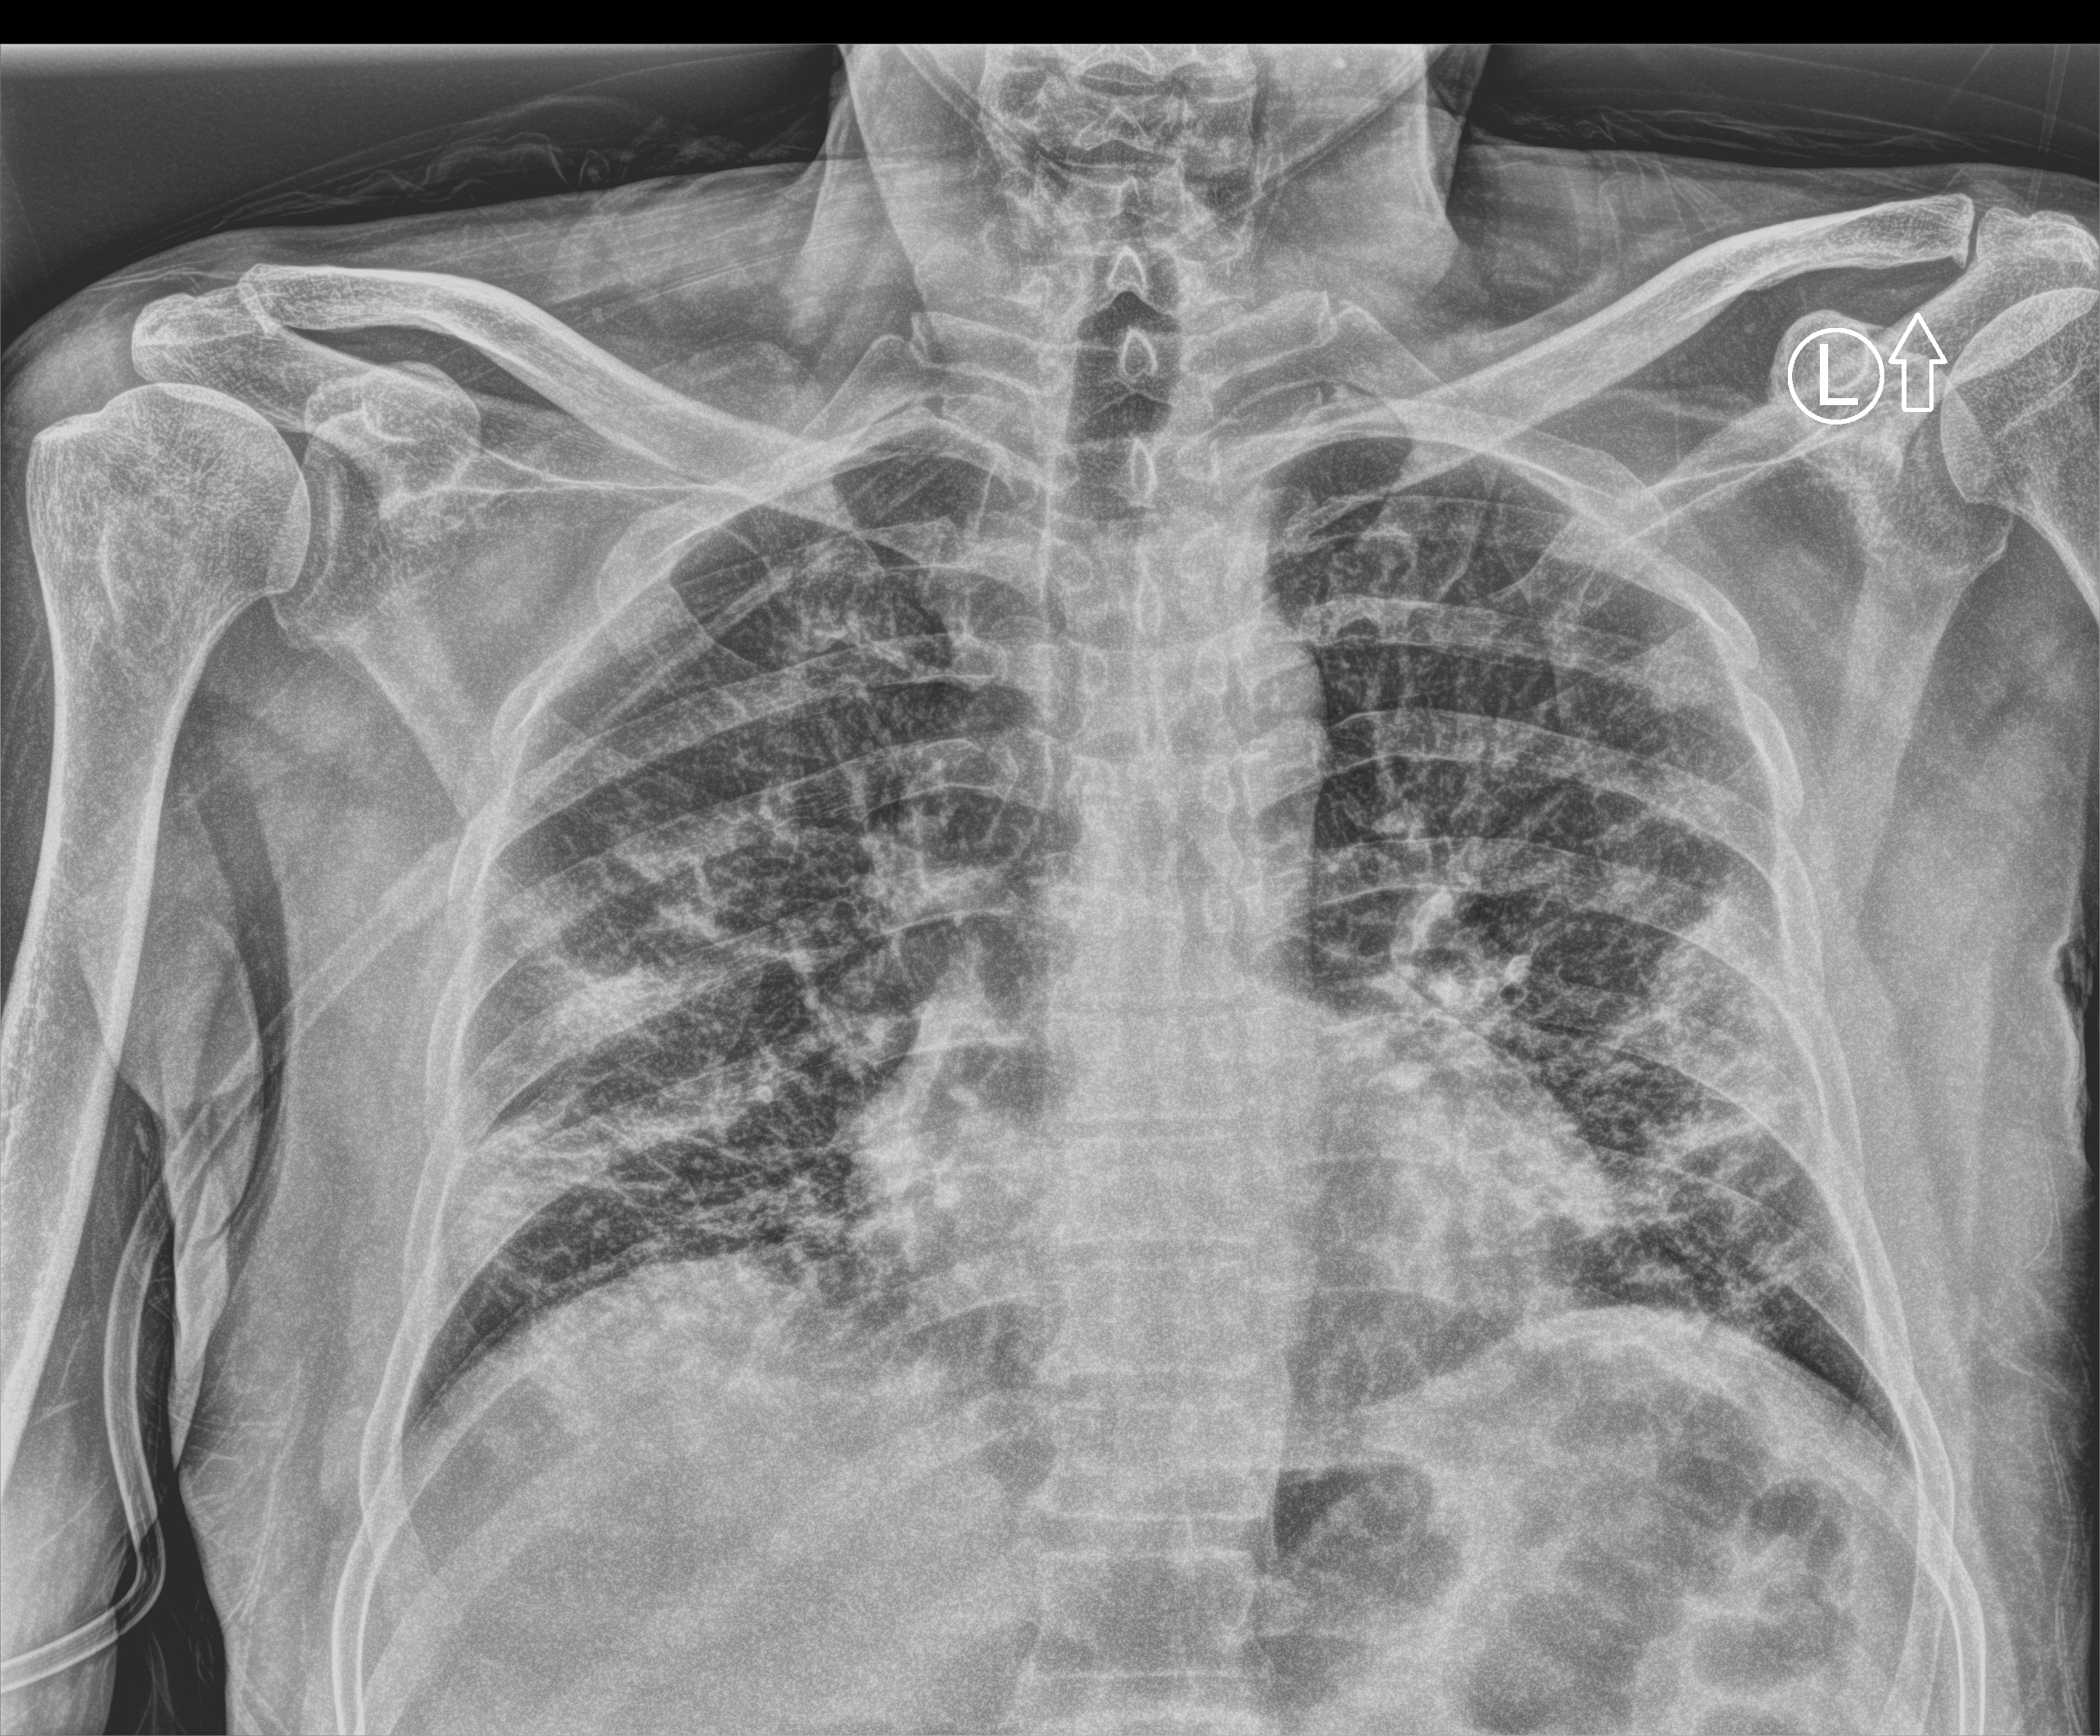
Chest X-ray (portable), anteroposterior (AP) projection. Patient hospitalised with COVID-19; male, aged 18–59 years.
Admission-level facts for this patient (not findings on this image; timing relative to this image not recorded): admitted to intensive care during this hospital stay: yes.